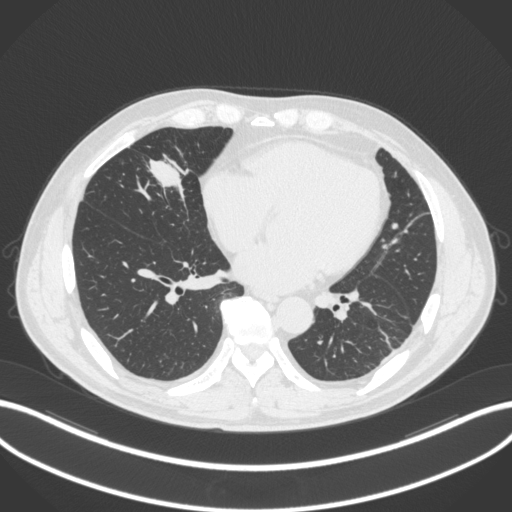
Chest CT, one axial slice. Position 106 of 399 along the scan axis. Reconstruction kernel B31f. Lung window (W 1500 / L -600 HU). 512 × 512 image matrix, field of view 400 × 400 mm. Male patient, age 59 years. Case-level facts recorded for this patient, not image findings: clinical TNM (as recorded): T2a N1 M0.
Annotated regions visible in this slice (rectangle marked by the reading radiologist):
- lung tumour (recorded histology: adenocarcinoma): box from (x=140, y=146) to (x=199, y=206) px